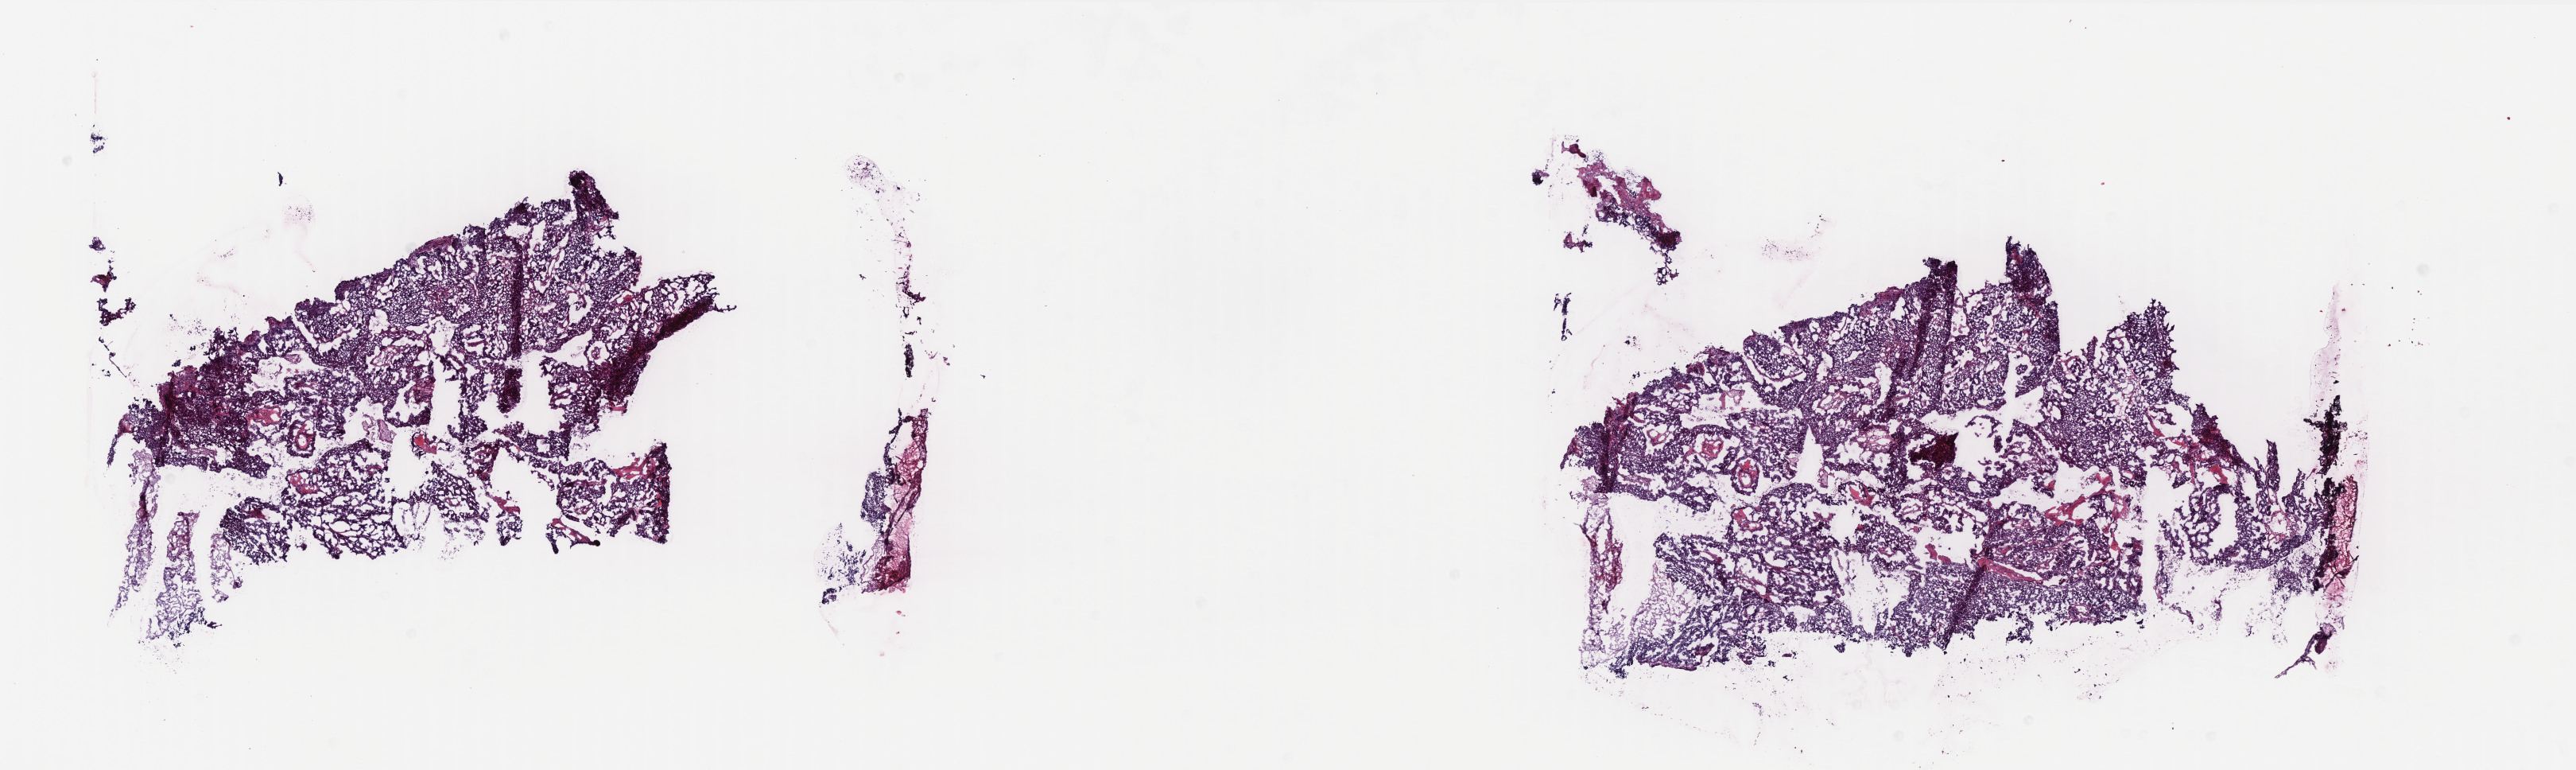
Digitized H&E tissue section (whole slide), low-resolution overview of the scanned area, about 26.0 x 7.8 mm (acquisition: 40x scan), frozen section from the top of the tissue portion, uterus, primary tumour sample. Female, age 54 years at initial diagnosis. Histologic grade: G3 (poorly differentiated). Pathologist review of this section (percent, as recorded): tumour cells 100%, tumour nuclei 90%, normal cells 0%, stromal cells 0%, necrosis 0%. Inflammatory infiltration, as recorded: lymphocyte infiltration 0%, monocyte infiltration 0%, neutrophil infiltration 0%.
FIGO stage: IA. Diagnosis: Endometrioid adenocarcinoma, NOS (endometrium). Lymph nodes positive (case pathology): 0 of 2 examined.